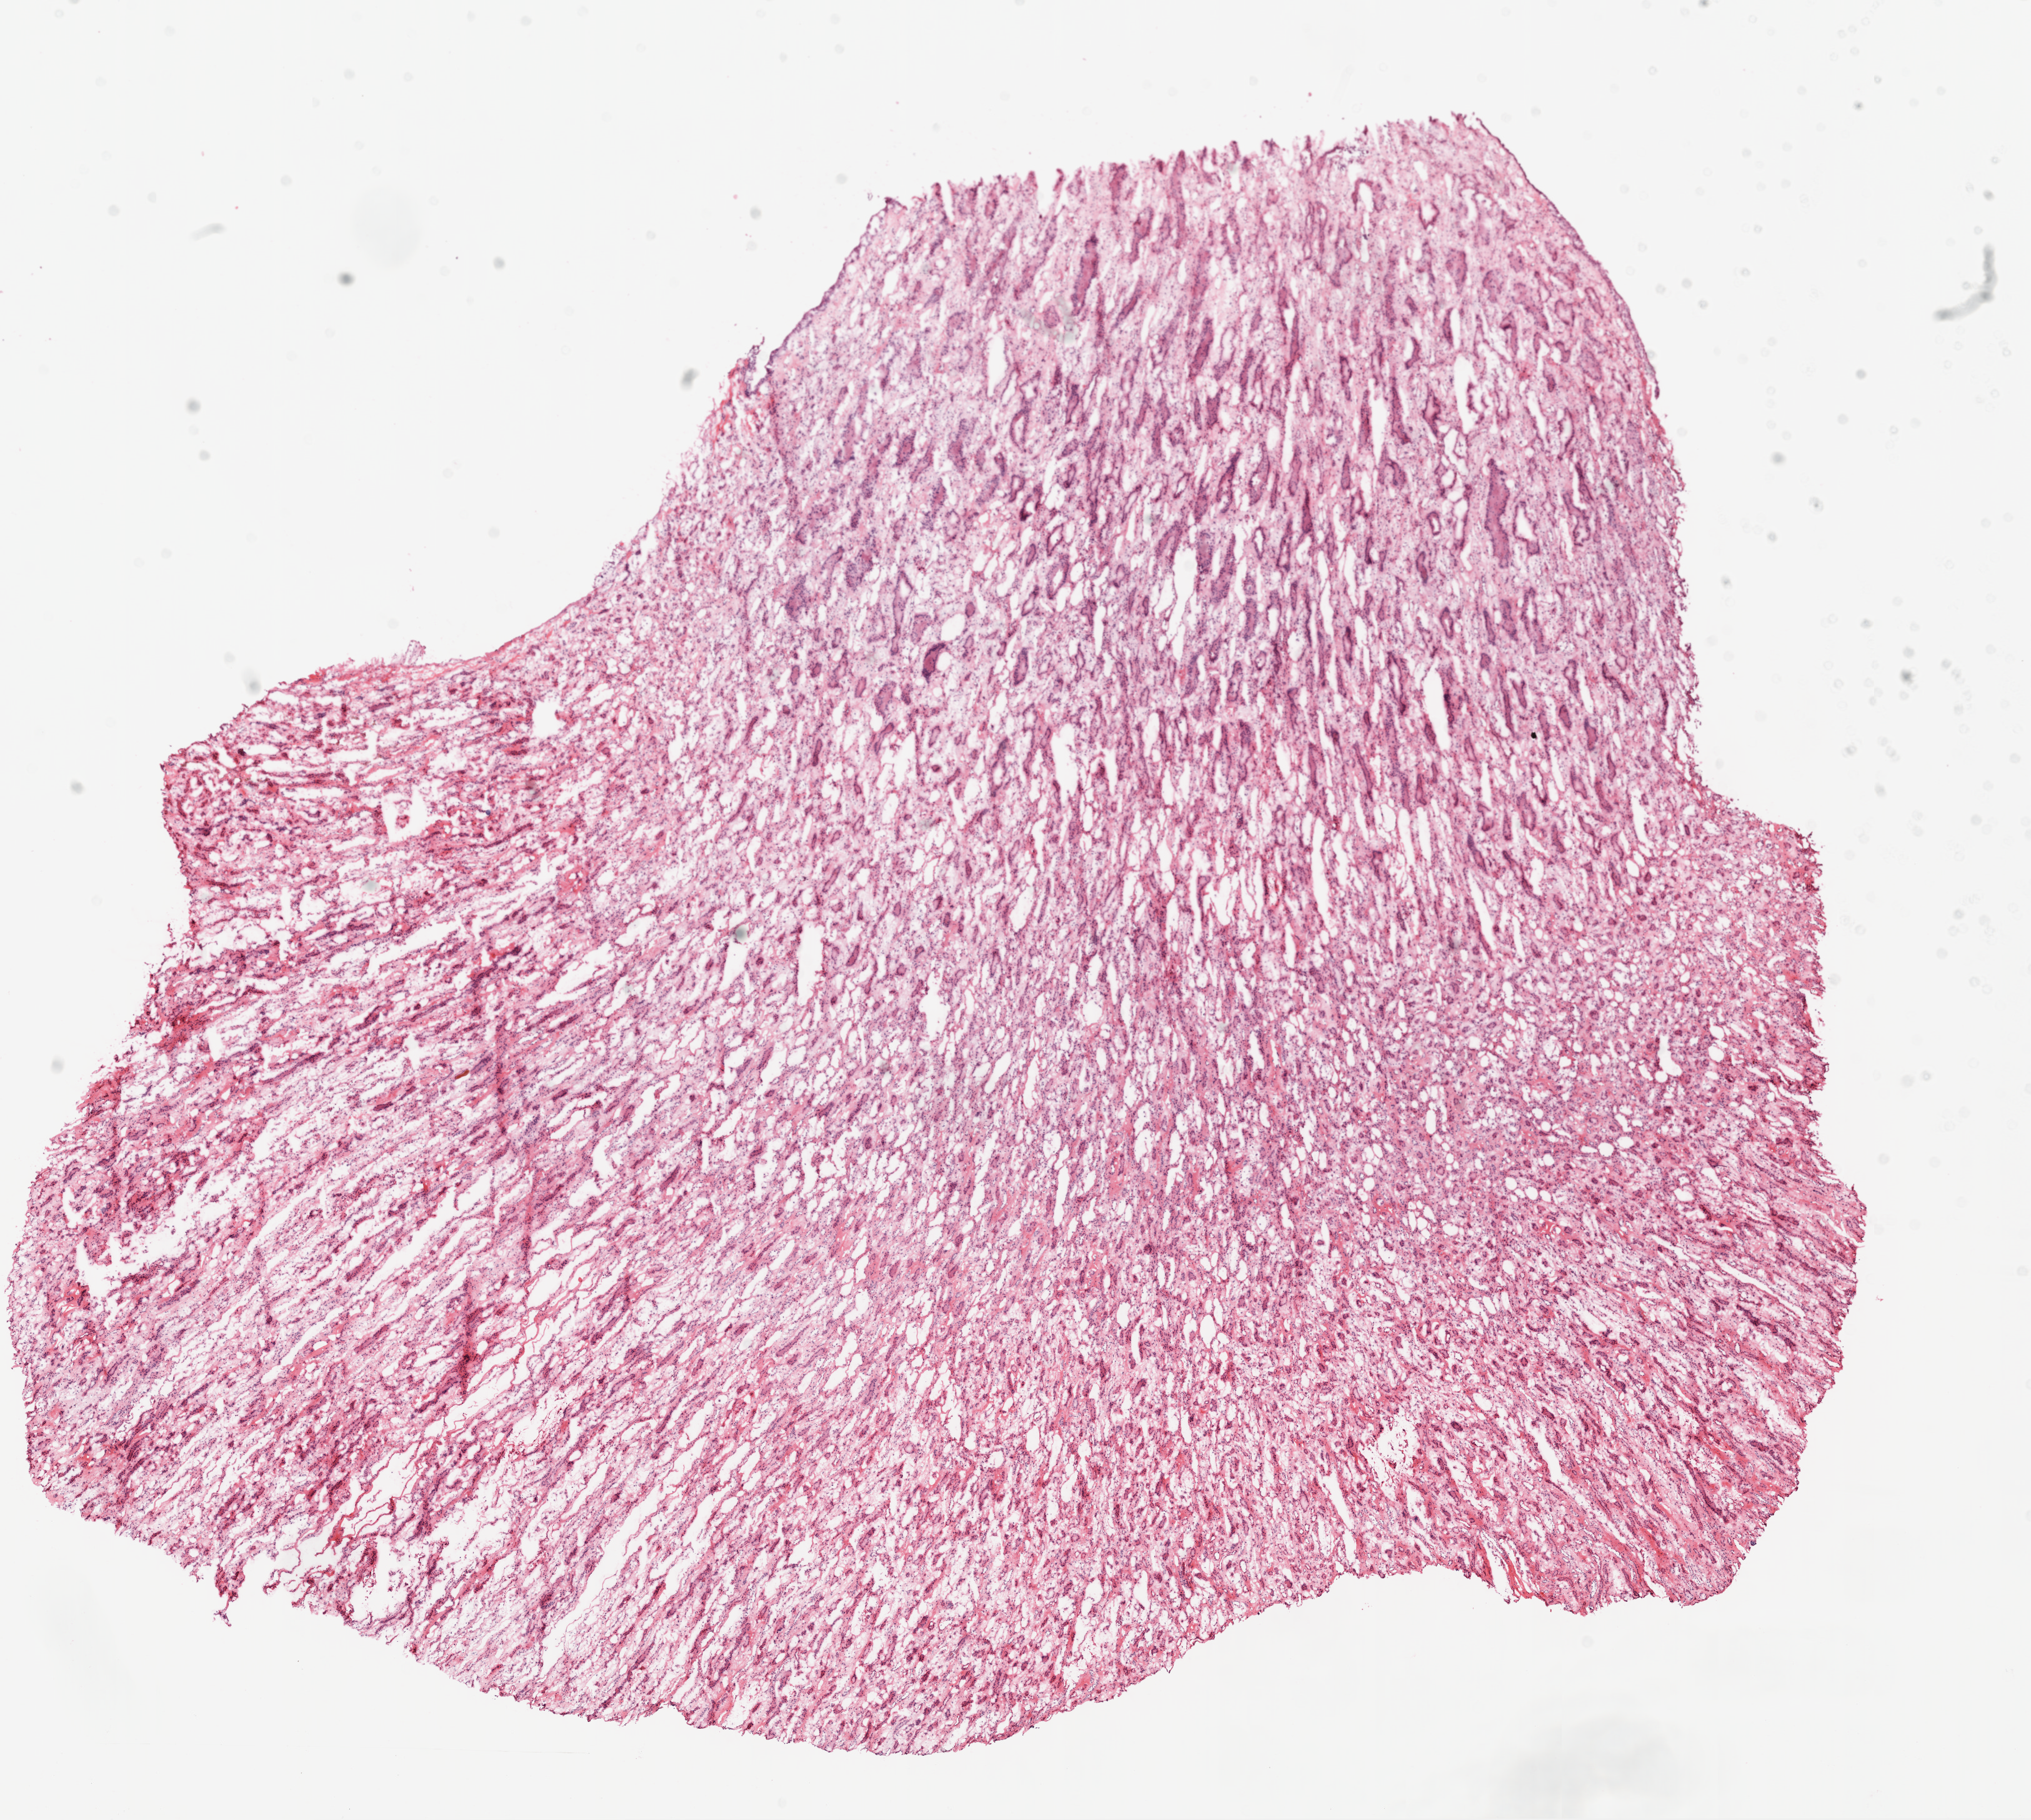
Digitized Hematoxylin and eosin (H&E) stained tissue section (whole slide) — low-resolution overview of the scanned area, about 13.0 x 11.7 mm. Frozen section. Solid tissue normal (non-tumour tissue) sample from the kidney. Female patient; age at initial diagnosis 62 years.
This section: solid tissue normal (non-tumour) sample from the same patient. Patient diagnosis: Clear cell adenocarcinoma, NOS.